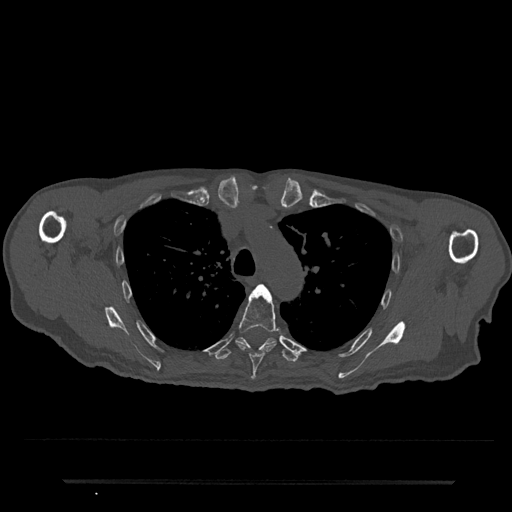
CT including the spine, one axial slice. Position 566 of 797 along the scan axis. Reconstruction kernel Br40s/3. Bone window (W 1800 / L 400 HU). 0.5 mm slice thickness. 512 × 512 image matrix, field of view 427 × 427 mm. Male patient, age 74 years. From the clinical record (not read from this slice): primary cancer: prostate.
Structures marked on this image (semi-automatically segmented with operator editing):
- T5 vertebra: bounding box (x1, y1, x2, y2) in pixels: (236, 284, 281, 380)
- T6 vertebra: (214, 337, 299, 362)